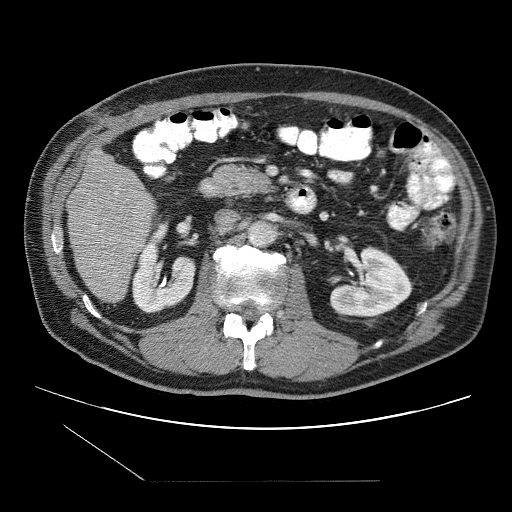
Contrast-enhanced abdominal CT (liver protocol), one axial slice; slice 32 of 109 in the series (ordered by position); reconstruction kernel STANDARD; 120 kVp; one of 2 acquisitions stored at this slice position; soft-tissue window (W 400 / L 40 HU); 512 × 512 image matrix, field of view 400 × 400 mm. From the clinical record (not read from this slice): diagnosis: hepatocellular carcinoma (patient treated with transarterial chemoembolisation; whether this scan precedes or follows treatment is not stated here); TNM stage (as recorded): Stage-IIIB.
Outlined on this slice (semi-automatic segmentation, software-assisted and operator-edited):
- liver parenchyma outside the tumour (the mass and vessels are separate outlines, so this box may not span the whole liver): bounding box (x1, y1, x2, y2) in pixels: (66, 148, 156, 302)
- liver vessels: (115, 191, 143, 233)